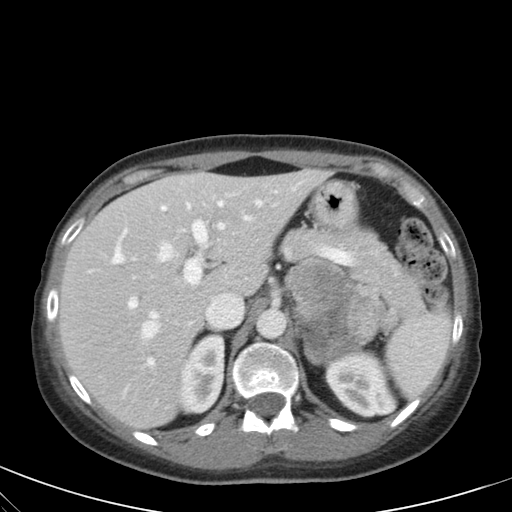
Contrast-enhanced abdominal CT, one axial slice; intravenous contrast given; soft-tissue window (W 400 / L 40 HU); 512 × 512 image matrix, field of view 350 × 350 mm. Patient: female, 28 years. Case-level facts recorded for this patient, not image findings: diagnosis: adrenocortical carcinoma; tumour side: left adrenal; tumour size at pathology: 7 cm; Ki-67 index: 40 %; stage (as recorded): 4.
Outlined on this slice (semi-automatically segmented with operator editing):
- mass: bounding box [x1, y1, x2, y2] px = [287, 259, 397, 362]